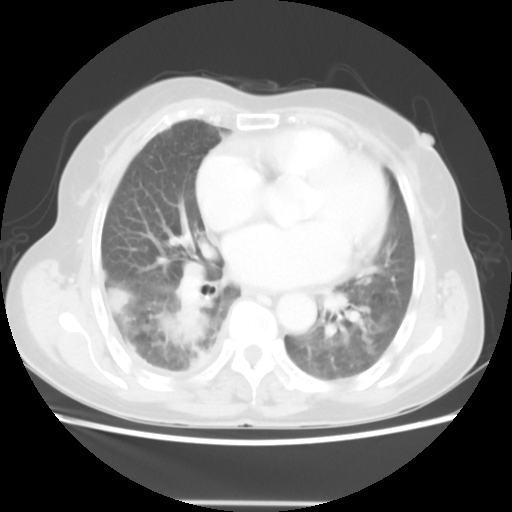
Chest CT, one axial slice; slice 24 of 52 in the series (ordered by position); reconstruction kernel STANDARD; lung window (W 1500 / L -600 HU); 5 mm slice thickness; 512 × 512 image matrix, field of view 337 × 337 mm. Female patient, age 67 years. From the clinical record (not read from this slice): clinical TNM (as recorded): T3 N1 M1.
Structures marked on this image (bounding box drawn by a radiologist):
- lung tumour (recorded histology: adenocarcinoma): box from (x=166, y=293) to (x=209, y=353) px